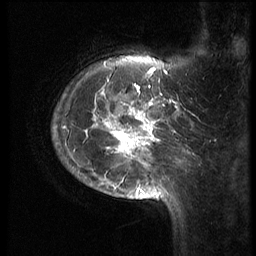
Breast MRI (dynamic contrast-enhanced), one sagittal slice; position 15 of 70 along the scan axis; 3 images stored at this slice position (order not interpretable as contrast timing); 1.5 T; TE 4.2 ms, TR 9 ms; 256 × 256 image matrix. Female patient, age 28 years. From the clinical record (not read from this slice): setting: breast cancer imaged before/during neoadjuvant chemotherapy.
Outlined on this slice (semi-automatically segmented with operator editing):
- analysis volume of interest (the breast-tissue region the enhancement analysis was run in; not a lesion): bounding box [x1, y1, x2, y2] px = [54, 42, 186, 215]
- tumour enhancement mask (voxels above the 140 % enhancement threshold inside the analysis volume of interest): [79, 62, 177, 201]